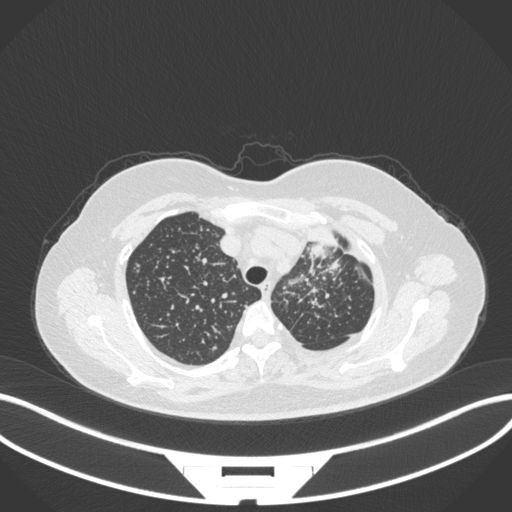
Chest CT, one axial slice. Position 269 of 348 along the scan axis. 120 kVp. Lung window (W 1500 / L -600 HU). 1 mm slice thickness. 512 × 512 image matrix, field of view 400 × 400 mm. Patient: female, 49 years. From the clinical record (not read from this slice): clinical TNM (as recorded): T1c N0 M1.
Structures marked on this image (rectangle marked by the reading radiologist):
- lung tumour (recorded histology: adenocarcinoma): bounding box [x1, y1, x2, y2] px = [307, 220, 342, 266]